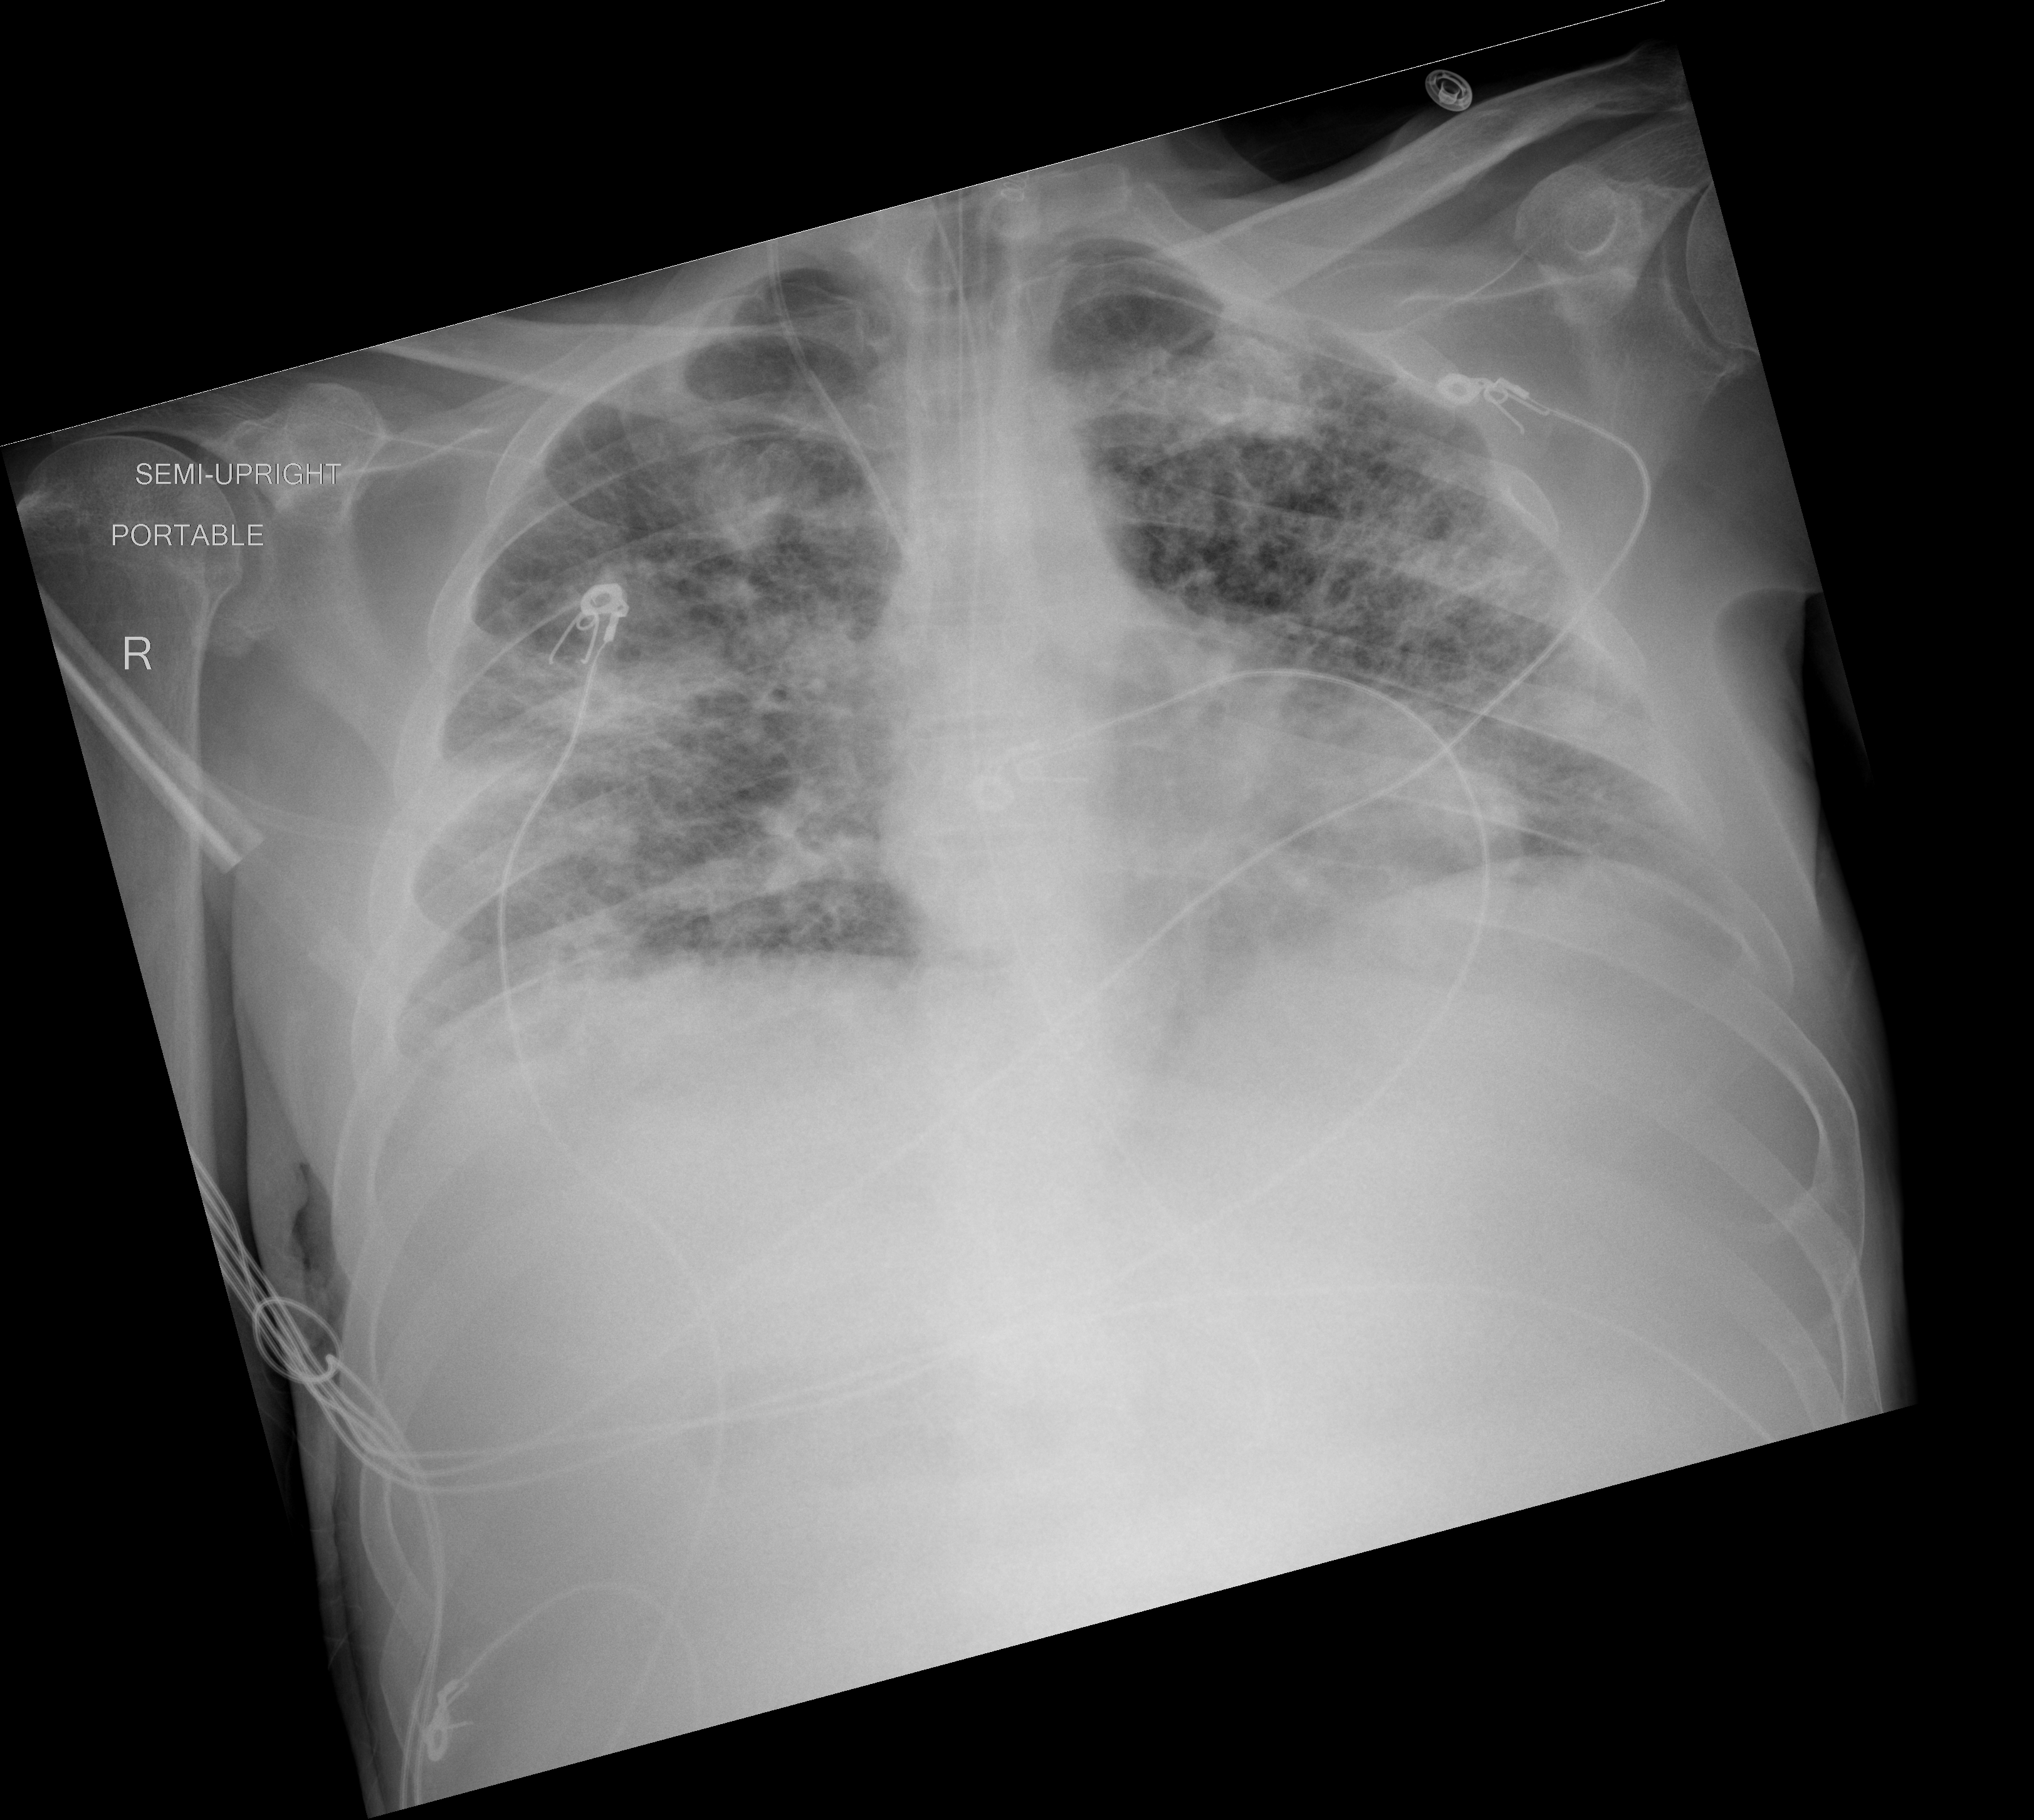
Chest X-ray (portable), AP projection. Male patient, age 54 years; imaged 0 days after the COVID-19 diagnosis.
Radiologist key findings (as recorded): Chronic lung disease/emphysema noted. Multifocal airspace opacities are noted throughout both lungs.